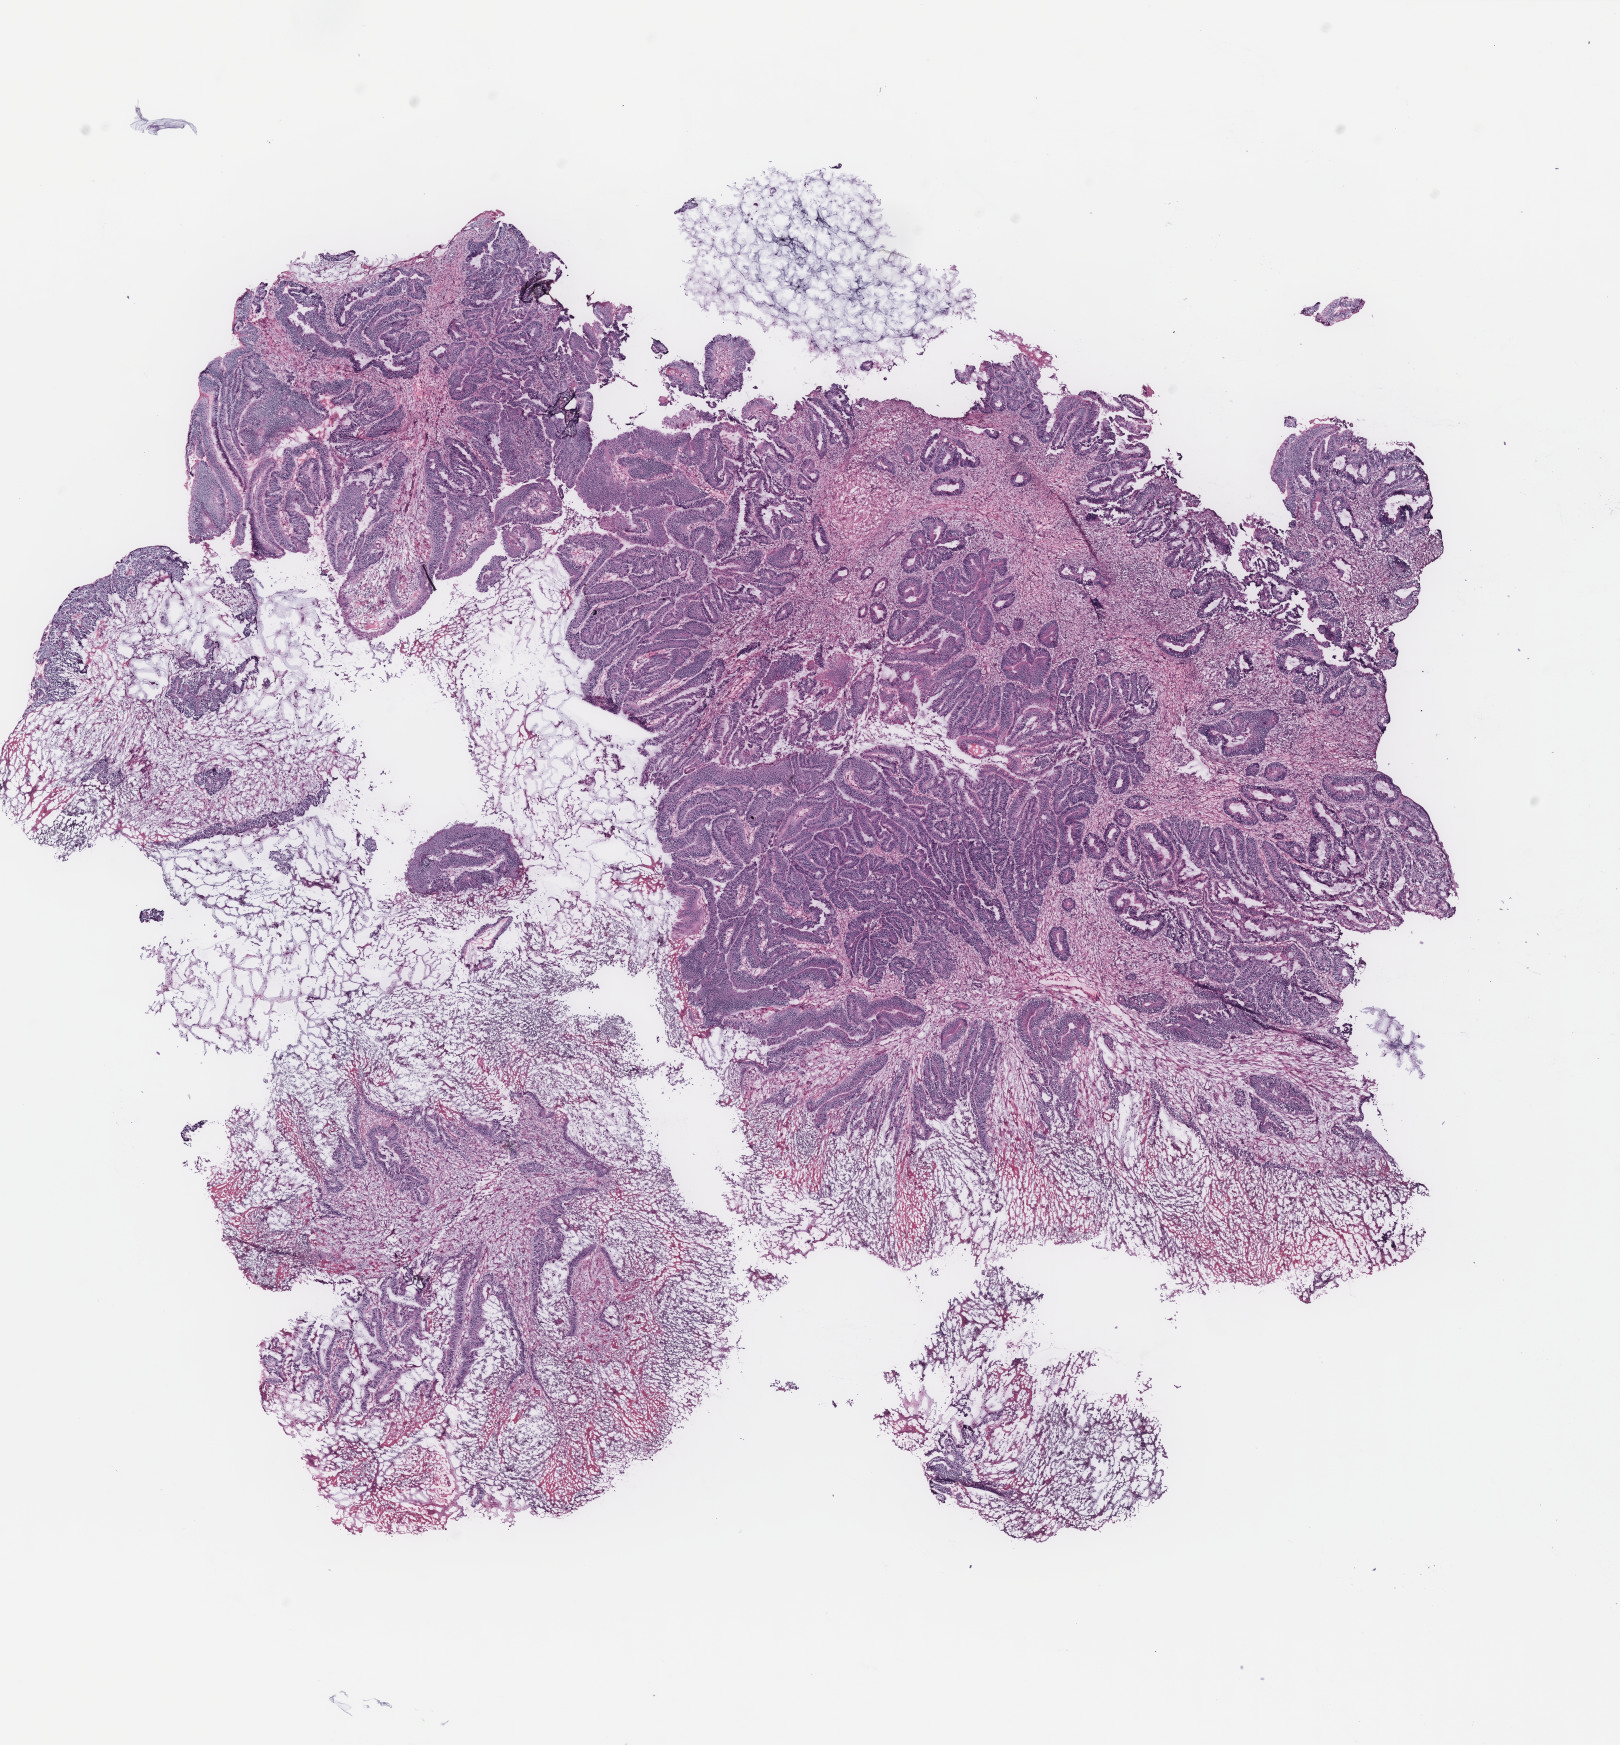
H&E whole-slide image, whole scanned area (about 13.0 x 14.0 mm, from a 40x scan) shown as a low-resolution overview, colon, tissue type not recorded. Female patient.
Patient diagnosis: Adenocarcinoma, NOS.